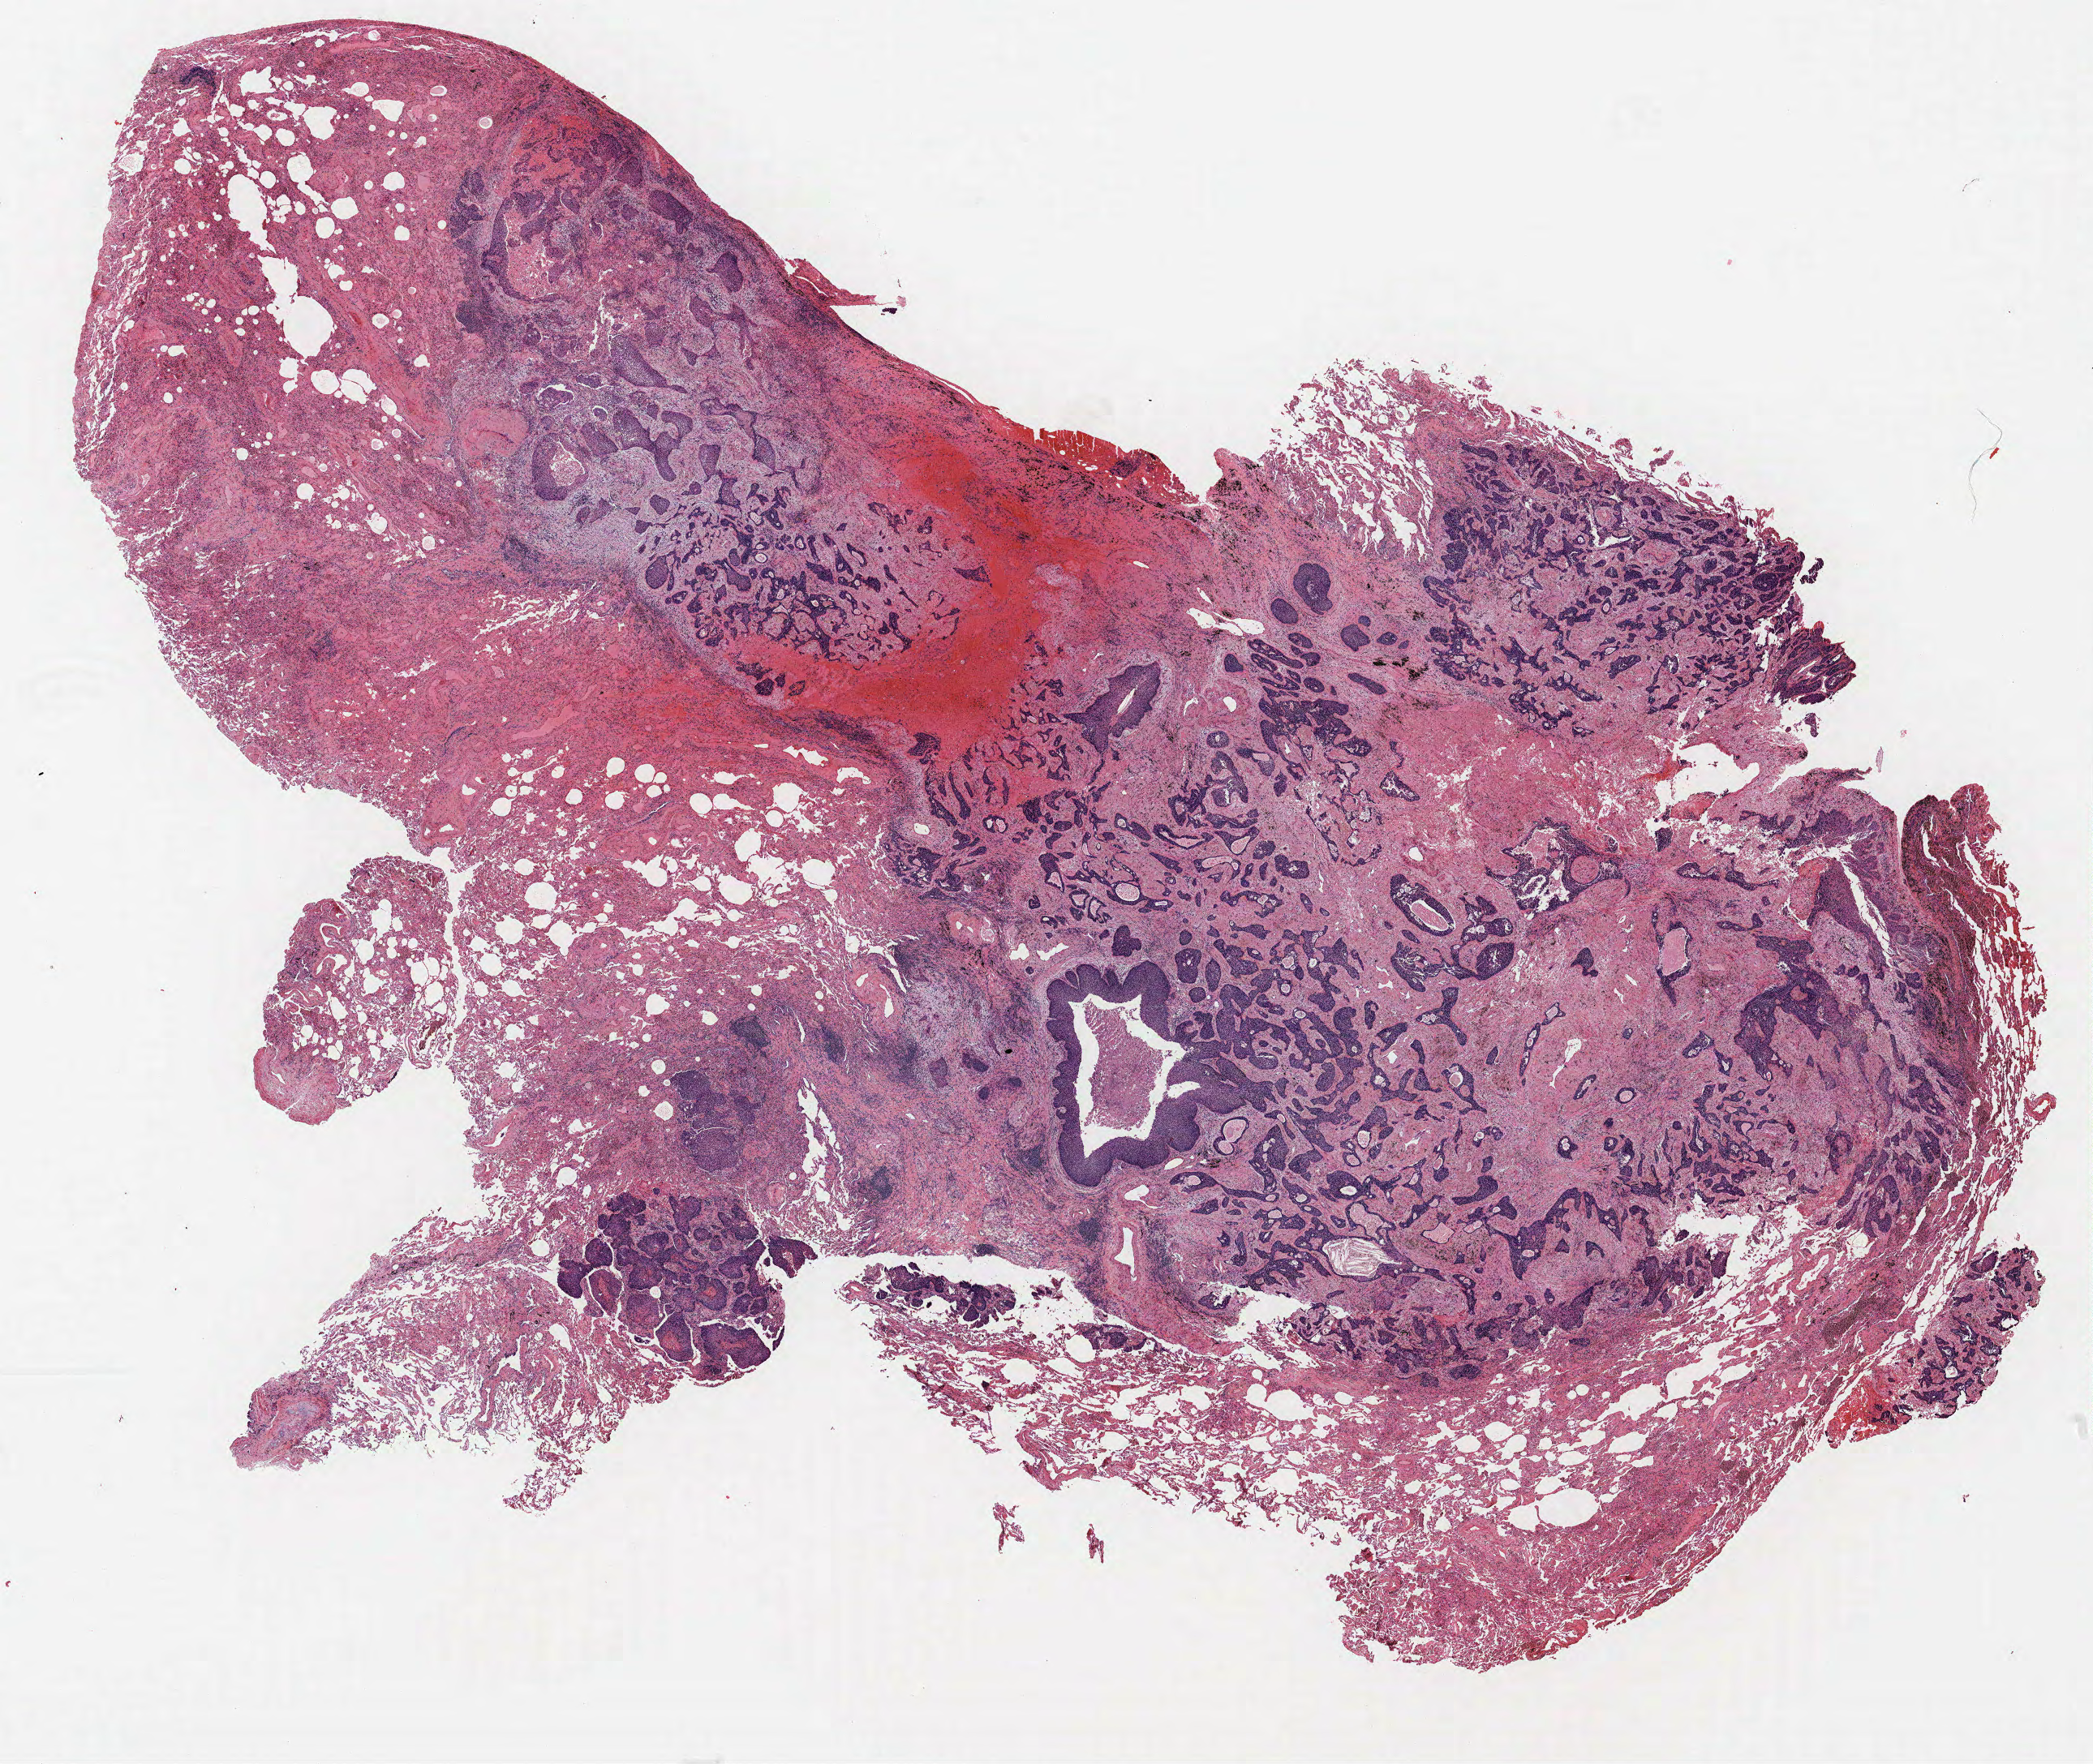
H&E-stained whole-slide image — shown as a low-resolution overview of the whole scanned area (about 20.6 x 17.4 mm, slide scanned at 40x), FFPE section, lung tissue. Female, age 66 at enrolment. Grade: poorly differentiated (G3).
Stage (AJCC 6th edition): IA. Primary tumour location (clinical record): right upper lobe, right middle lobe. Tumour size (pathology): 14 mm. Participant's lung-cancer diagnosis: Squamous cell carcinoma, keratinizing, NOS.